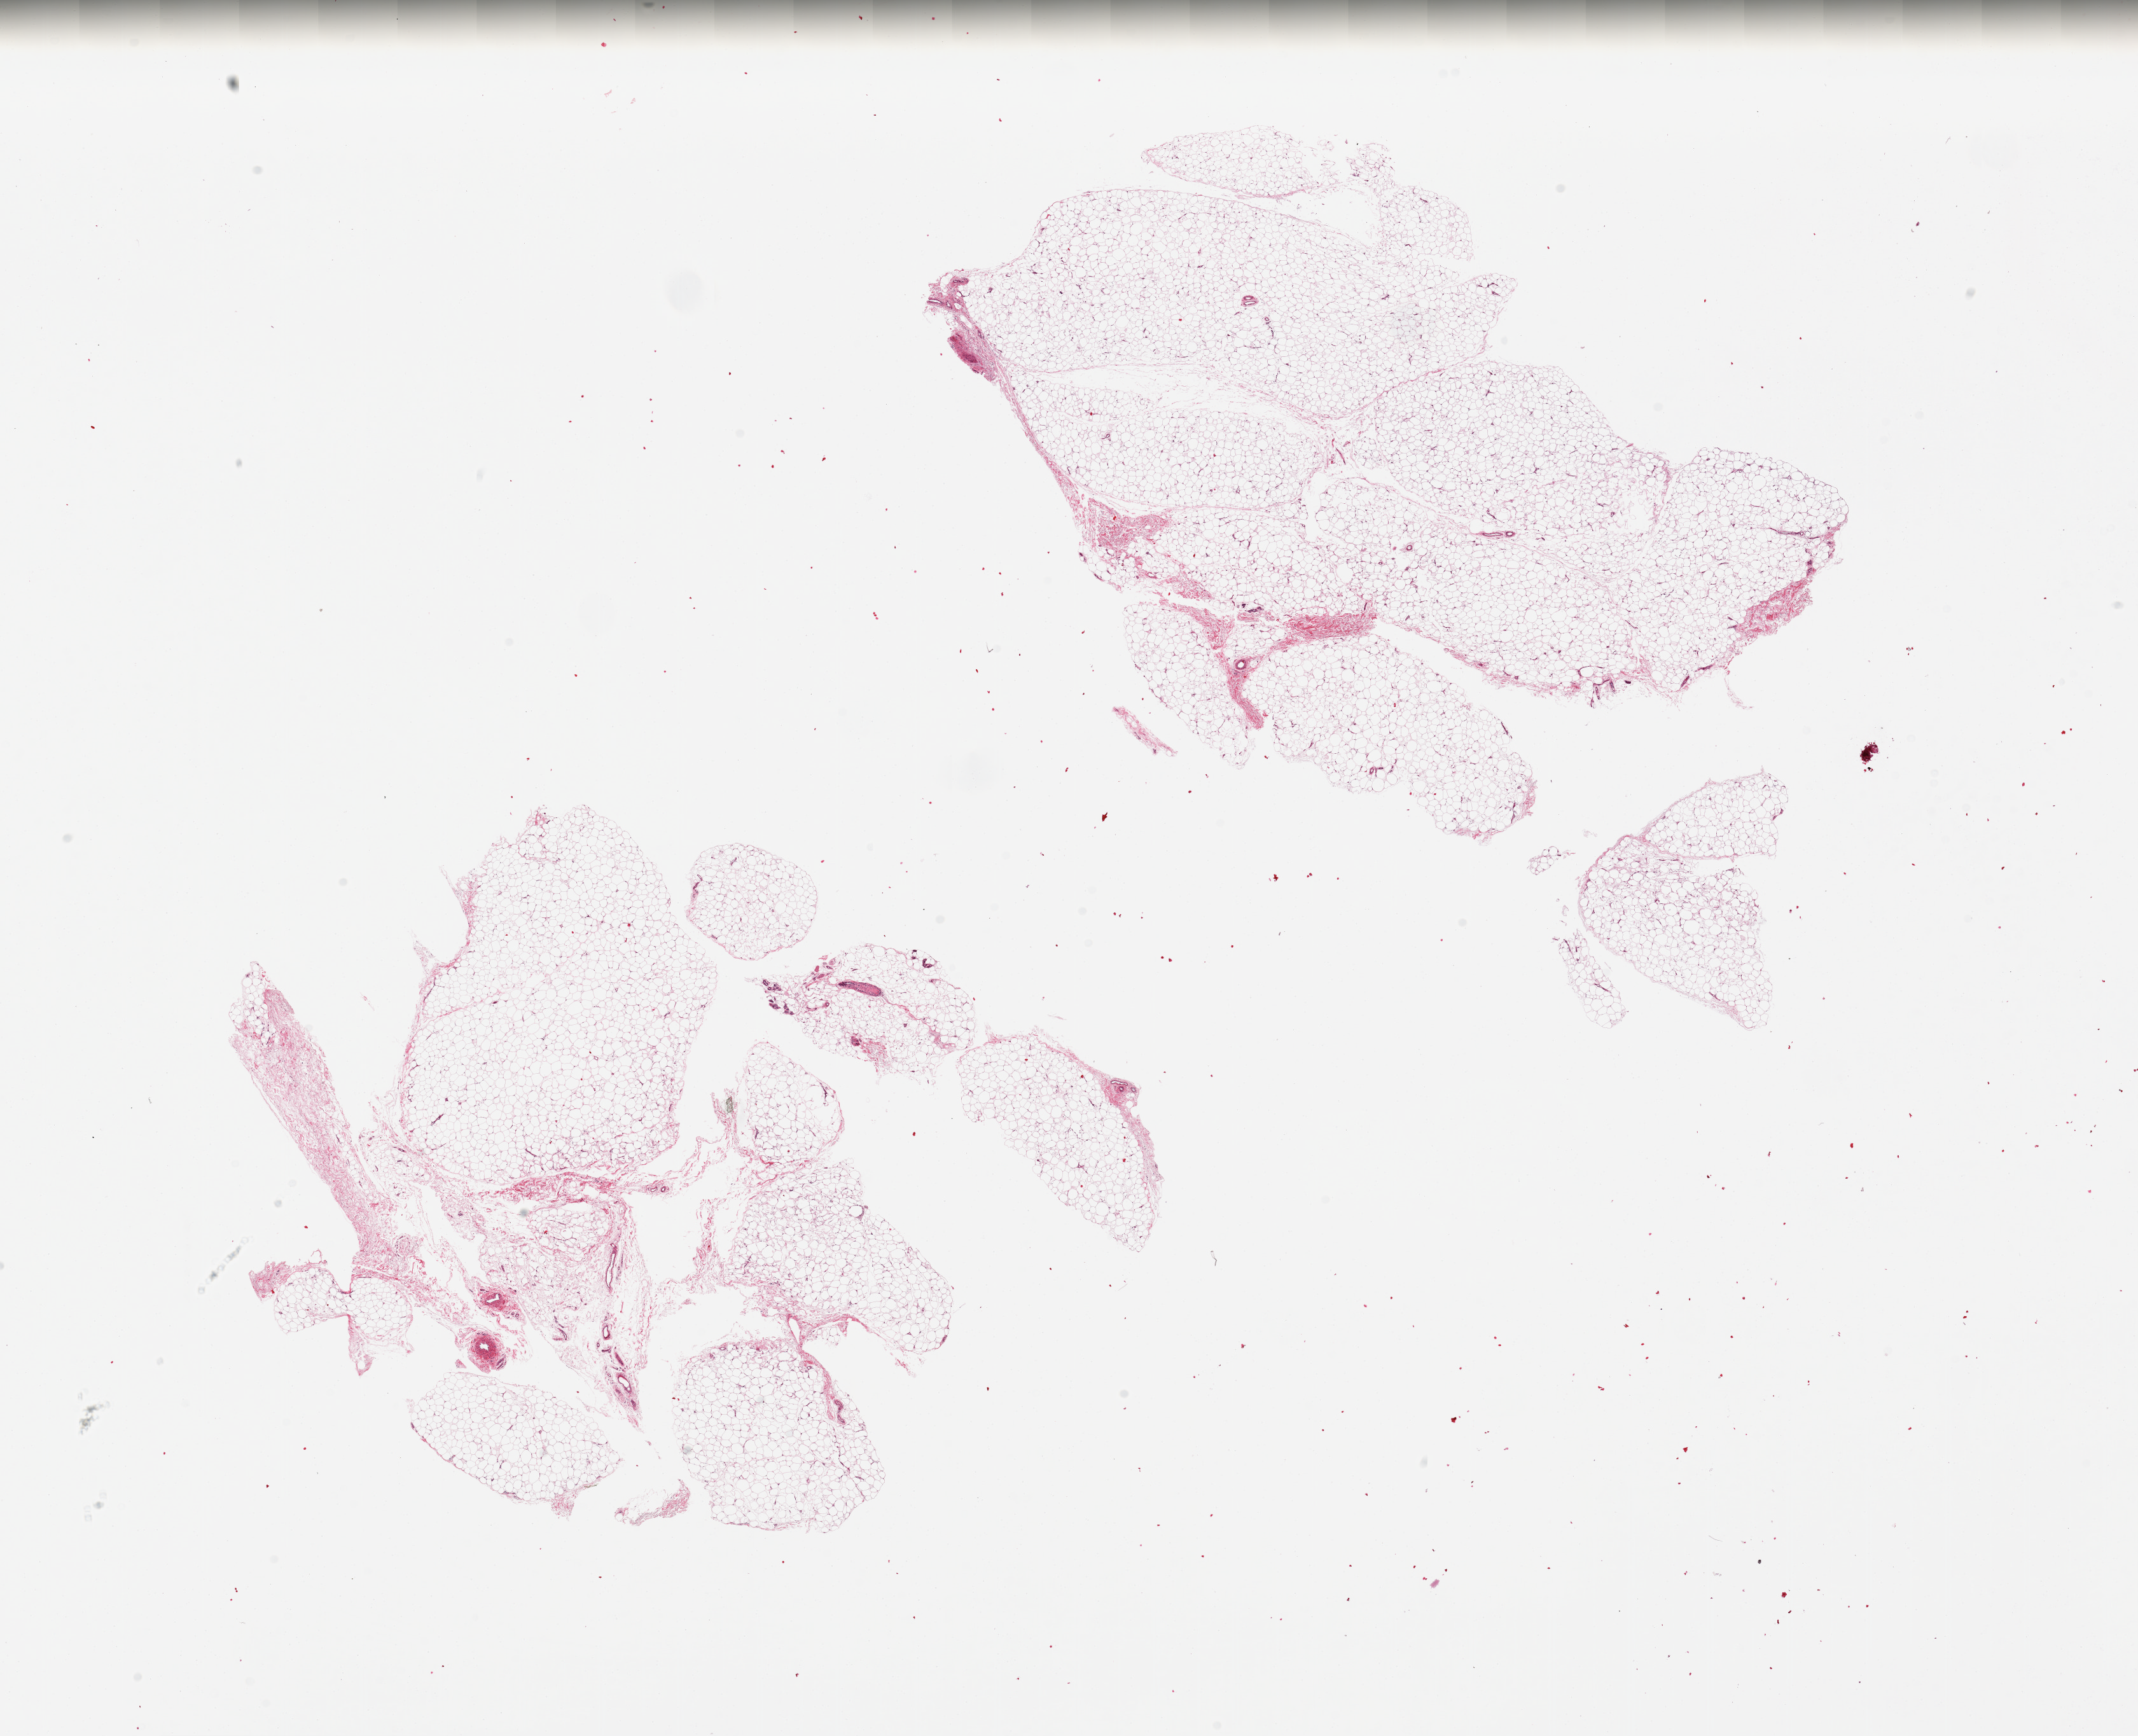
Whole-slide image, haematoxylin and eosin stain, a low-resolution overview of the entire scanned area, about 26.6 x 21.6 mm. PAXgene-fixed, paraffin-embedded tissue. Target tissue: adipose tissue. Tissue donor sample. Female donor.
- reviewer comment on this tissue sample: 2 pieces, ~5-10% fibrous/fascial tissue